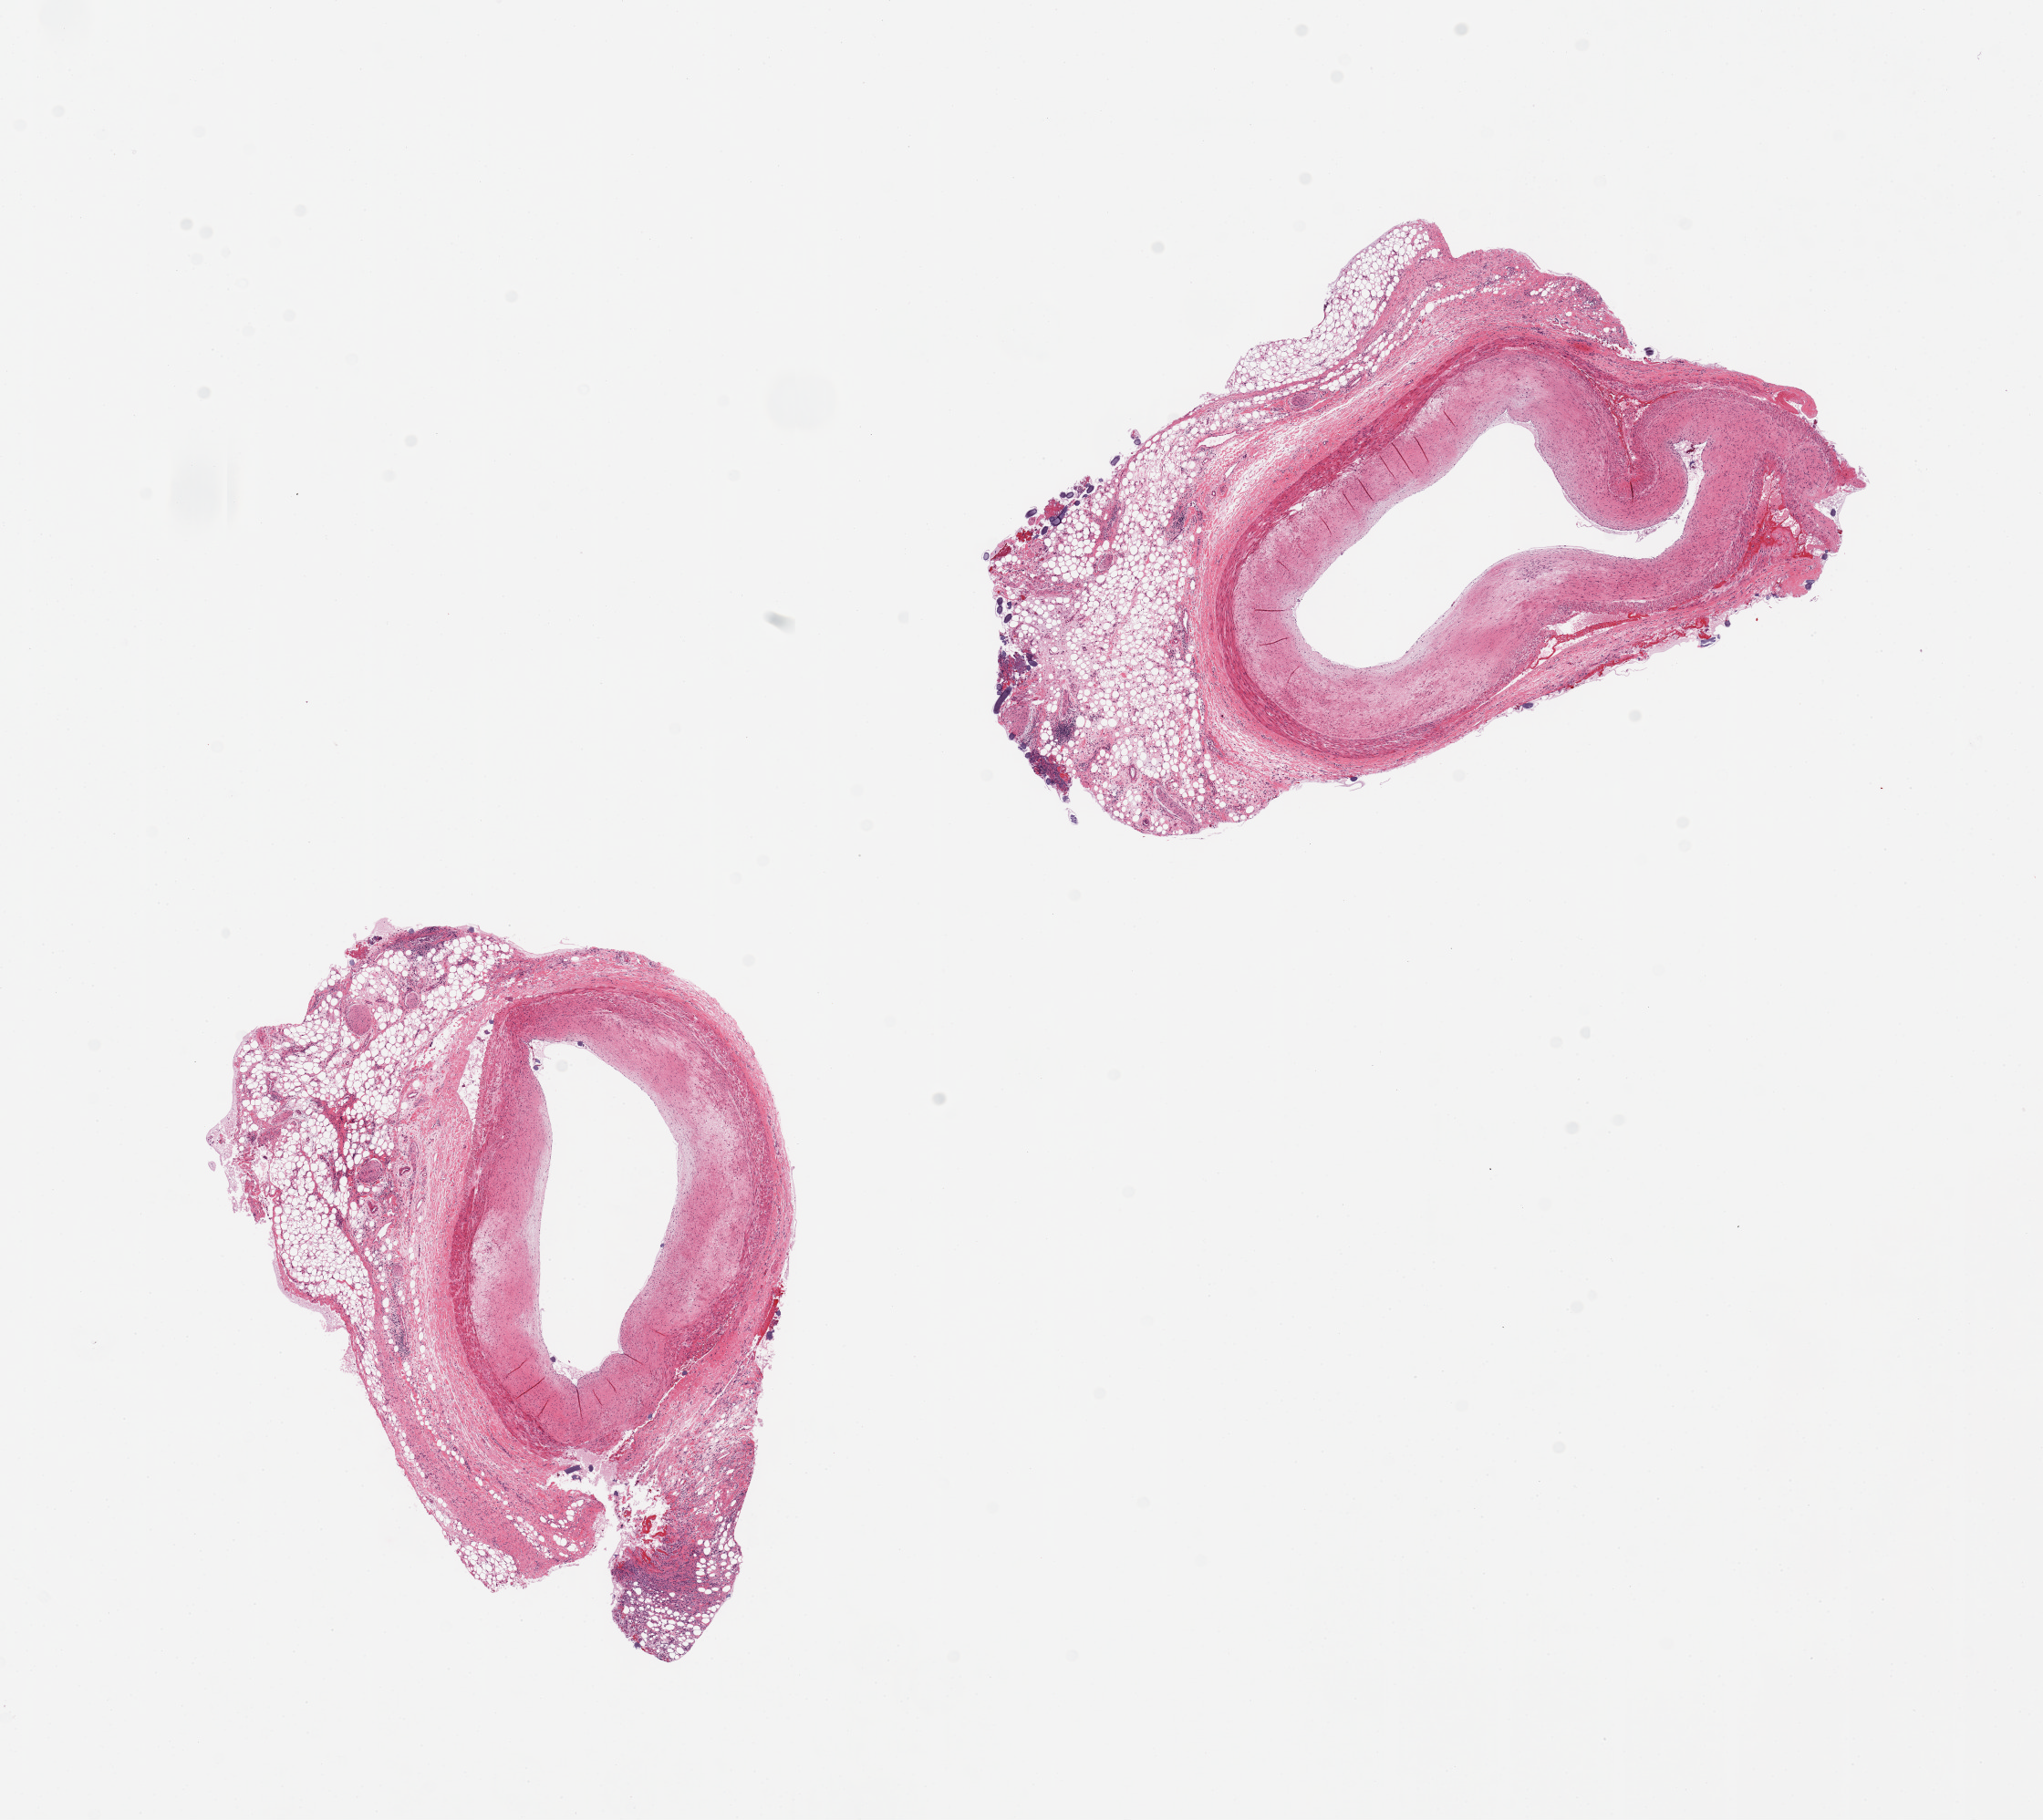
Digitized haematoxylin and eosin-stained section — whole scanned area (about 17.7 x 15.8 mm) shown as a low-resolution overview; PAXgene-fixed, paraffin-embedded tissue; sampled site (target tissue): coronary artery; donor tissue sample. Donor sex: male.
• reviewer comment on this tissue sample: 2 pieces; patent lumens, but atherosclerotic; 40% adjacent fat